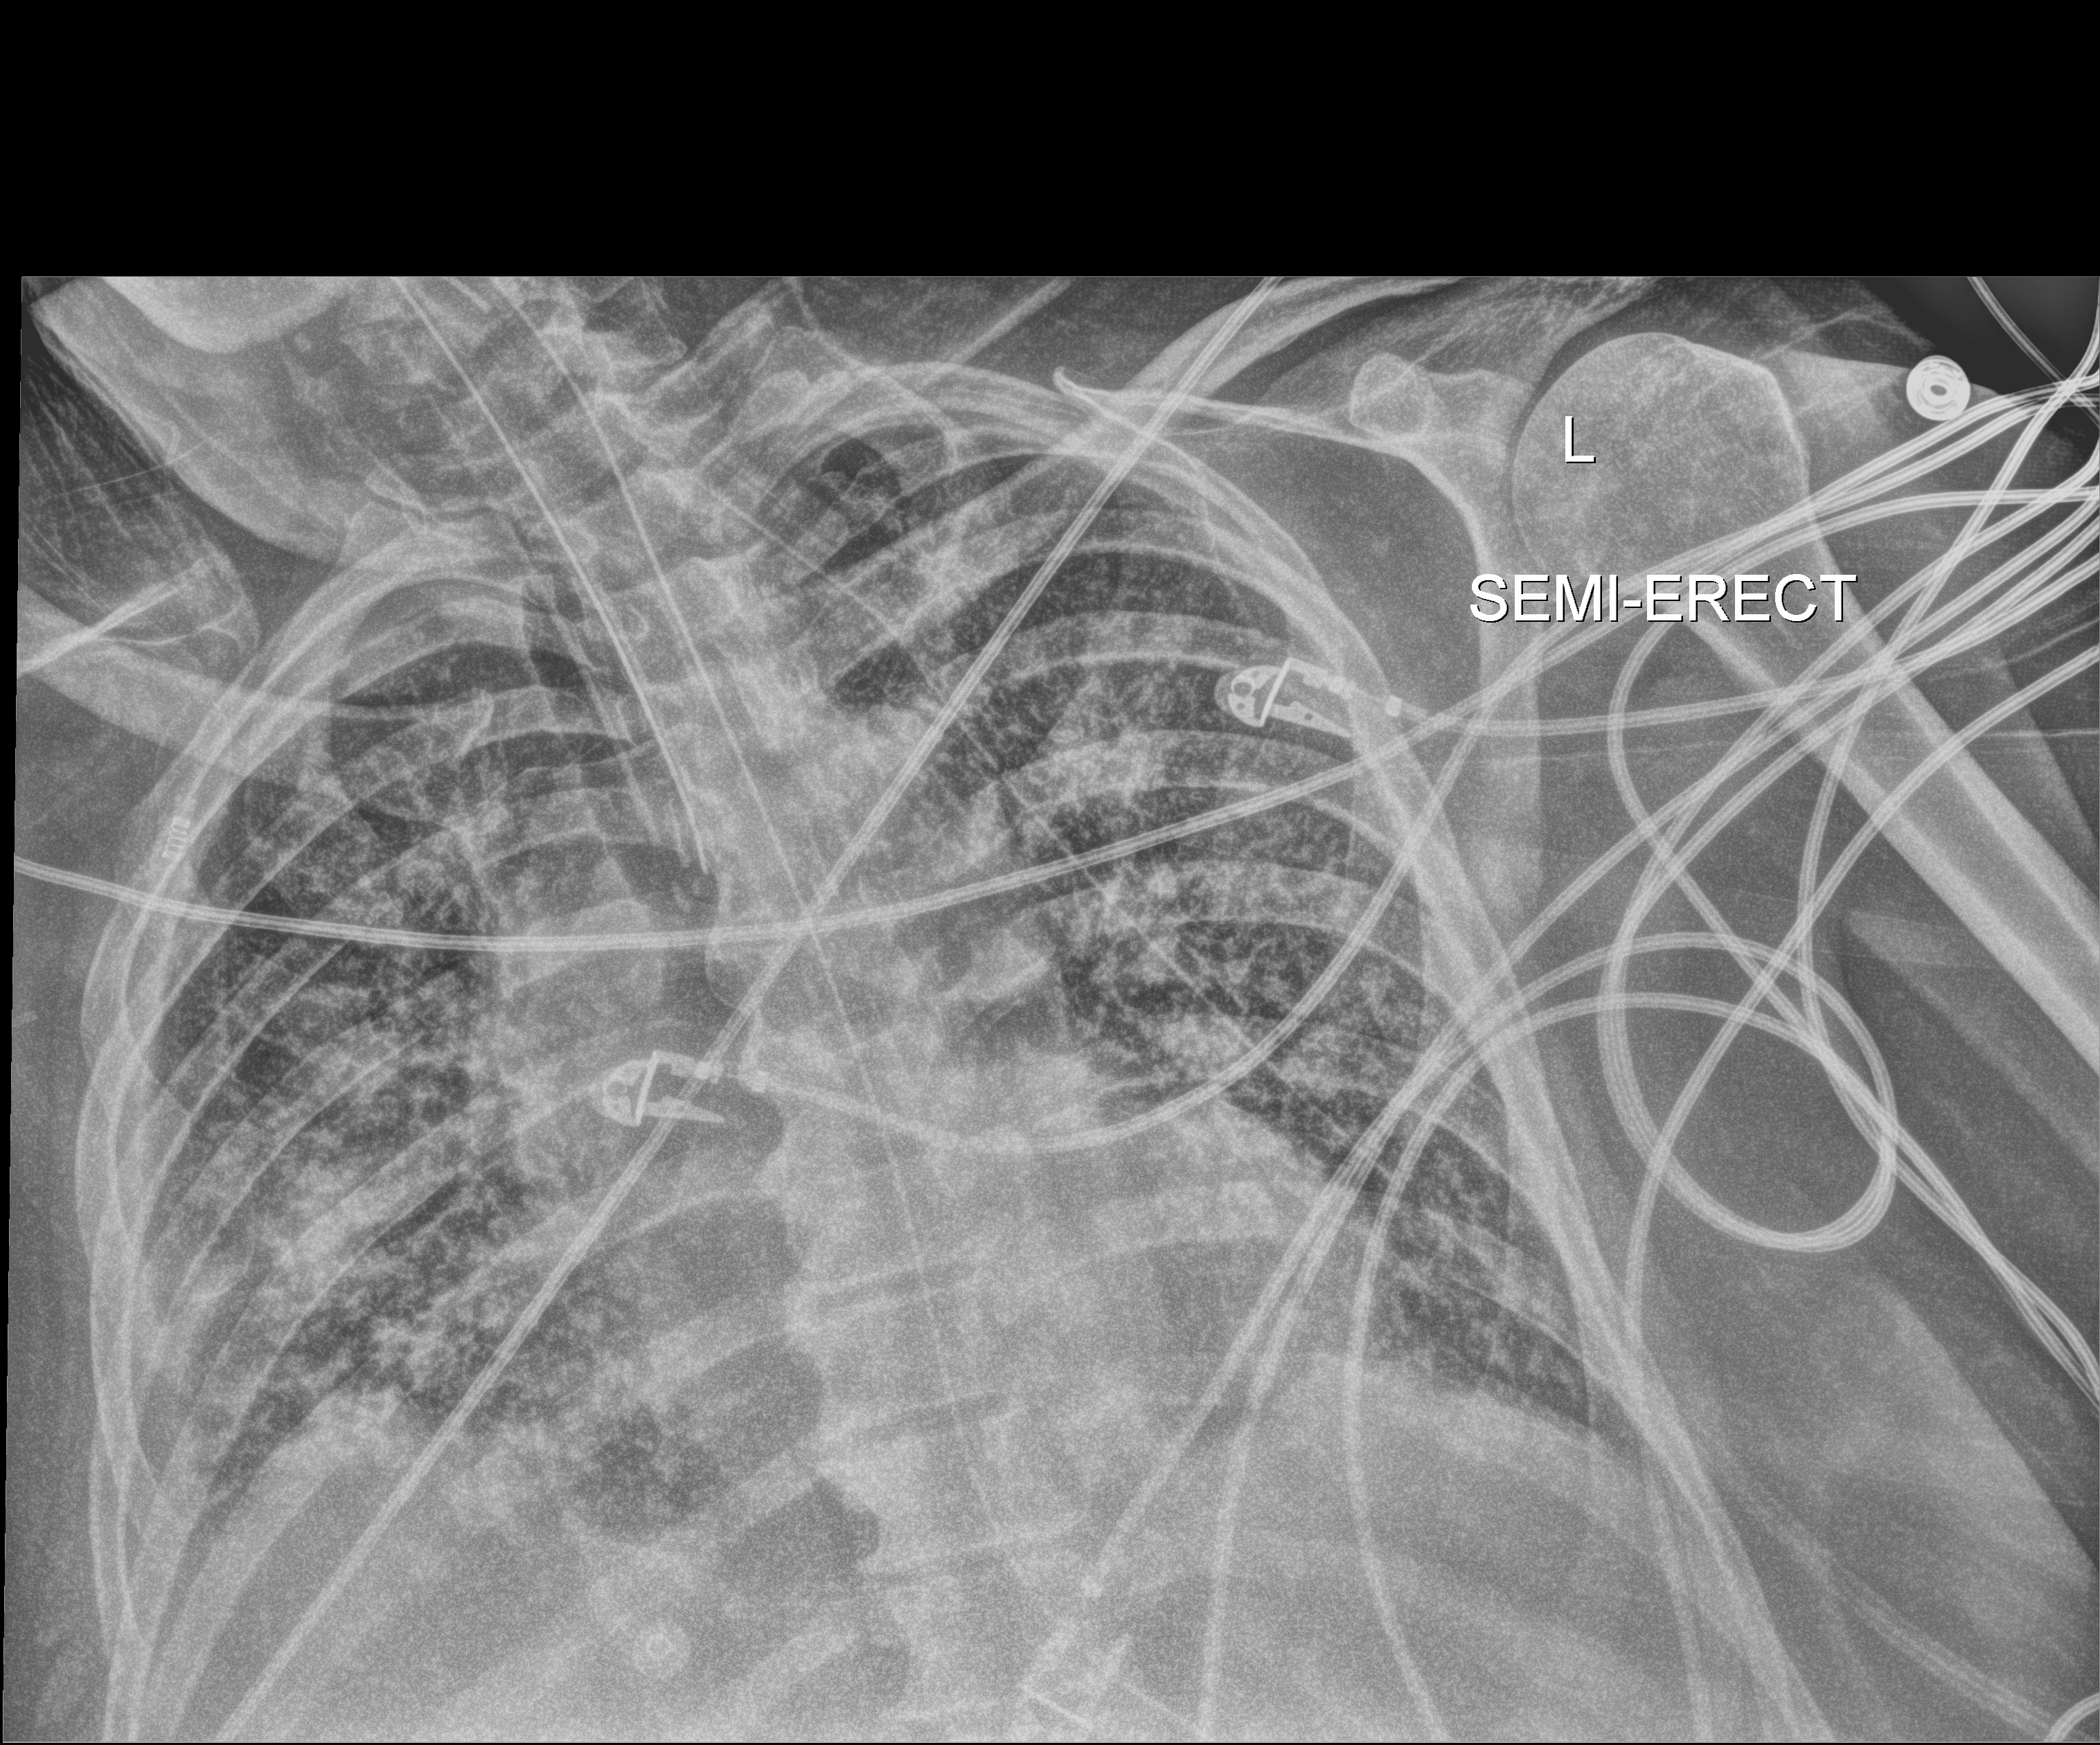
Portable chest radiograph; anteroposterior (AP) projection. Male patient hospitalised with COVID-19, age 60–74 years.
From the hospital-stay record, not from the radiograph (when in the stay this image was taken is not recorded): other chronic lung disease (admission record): no.